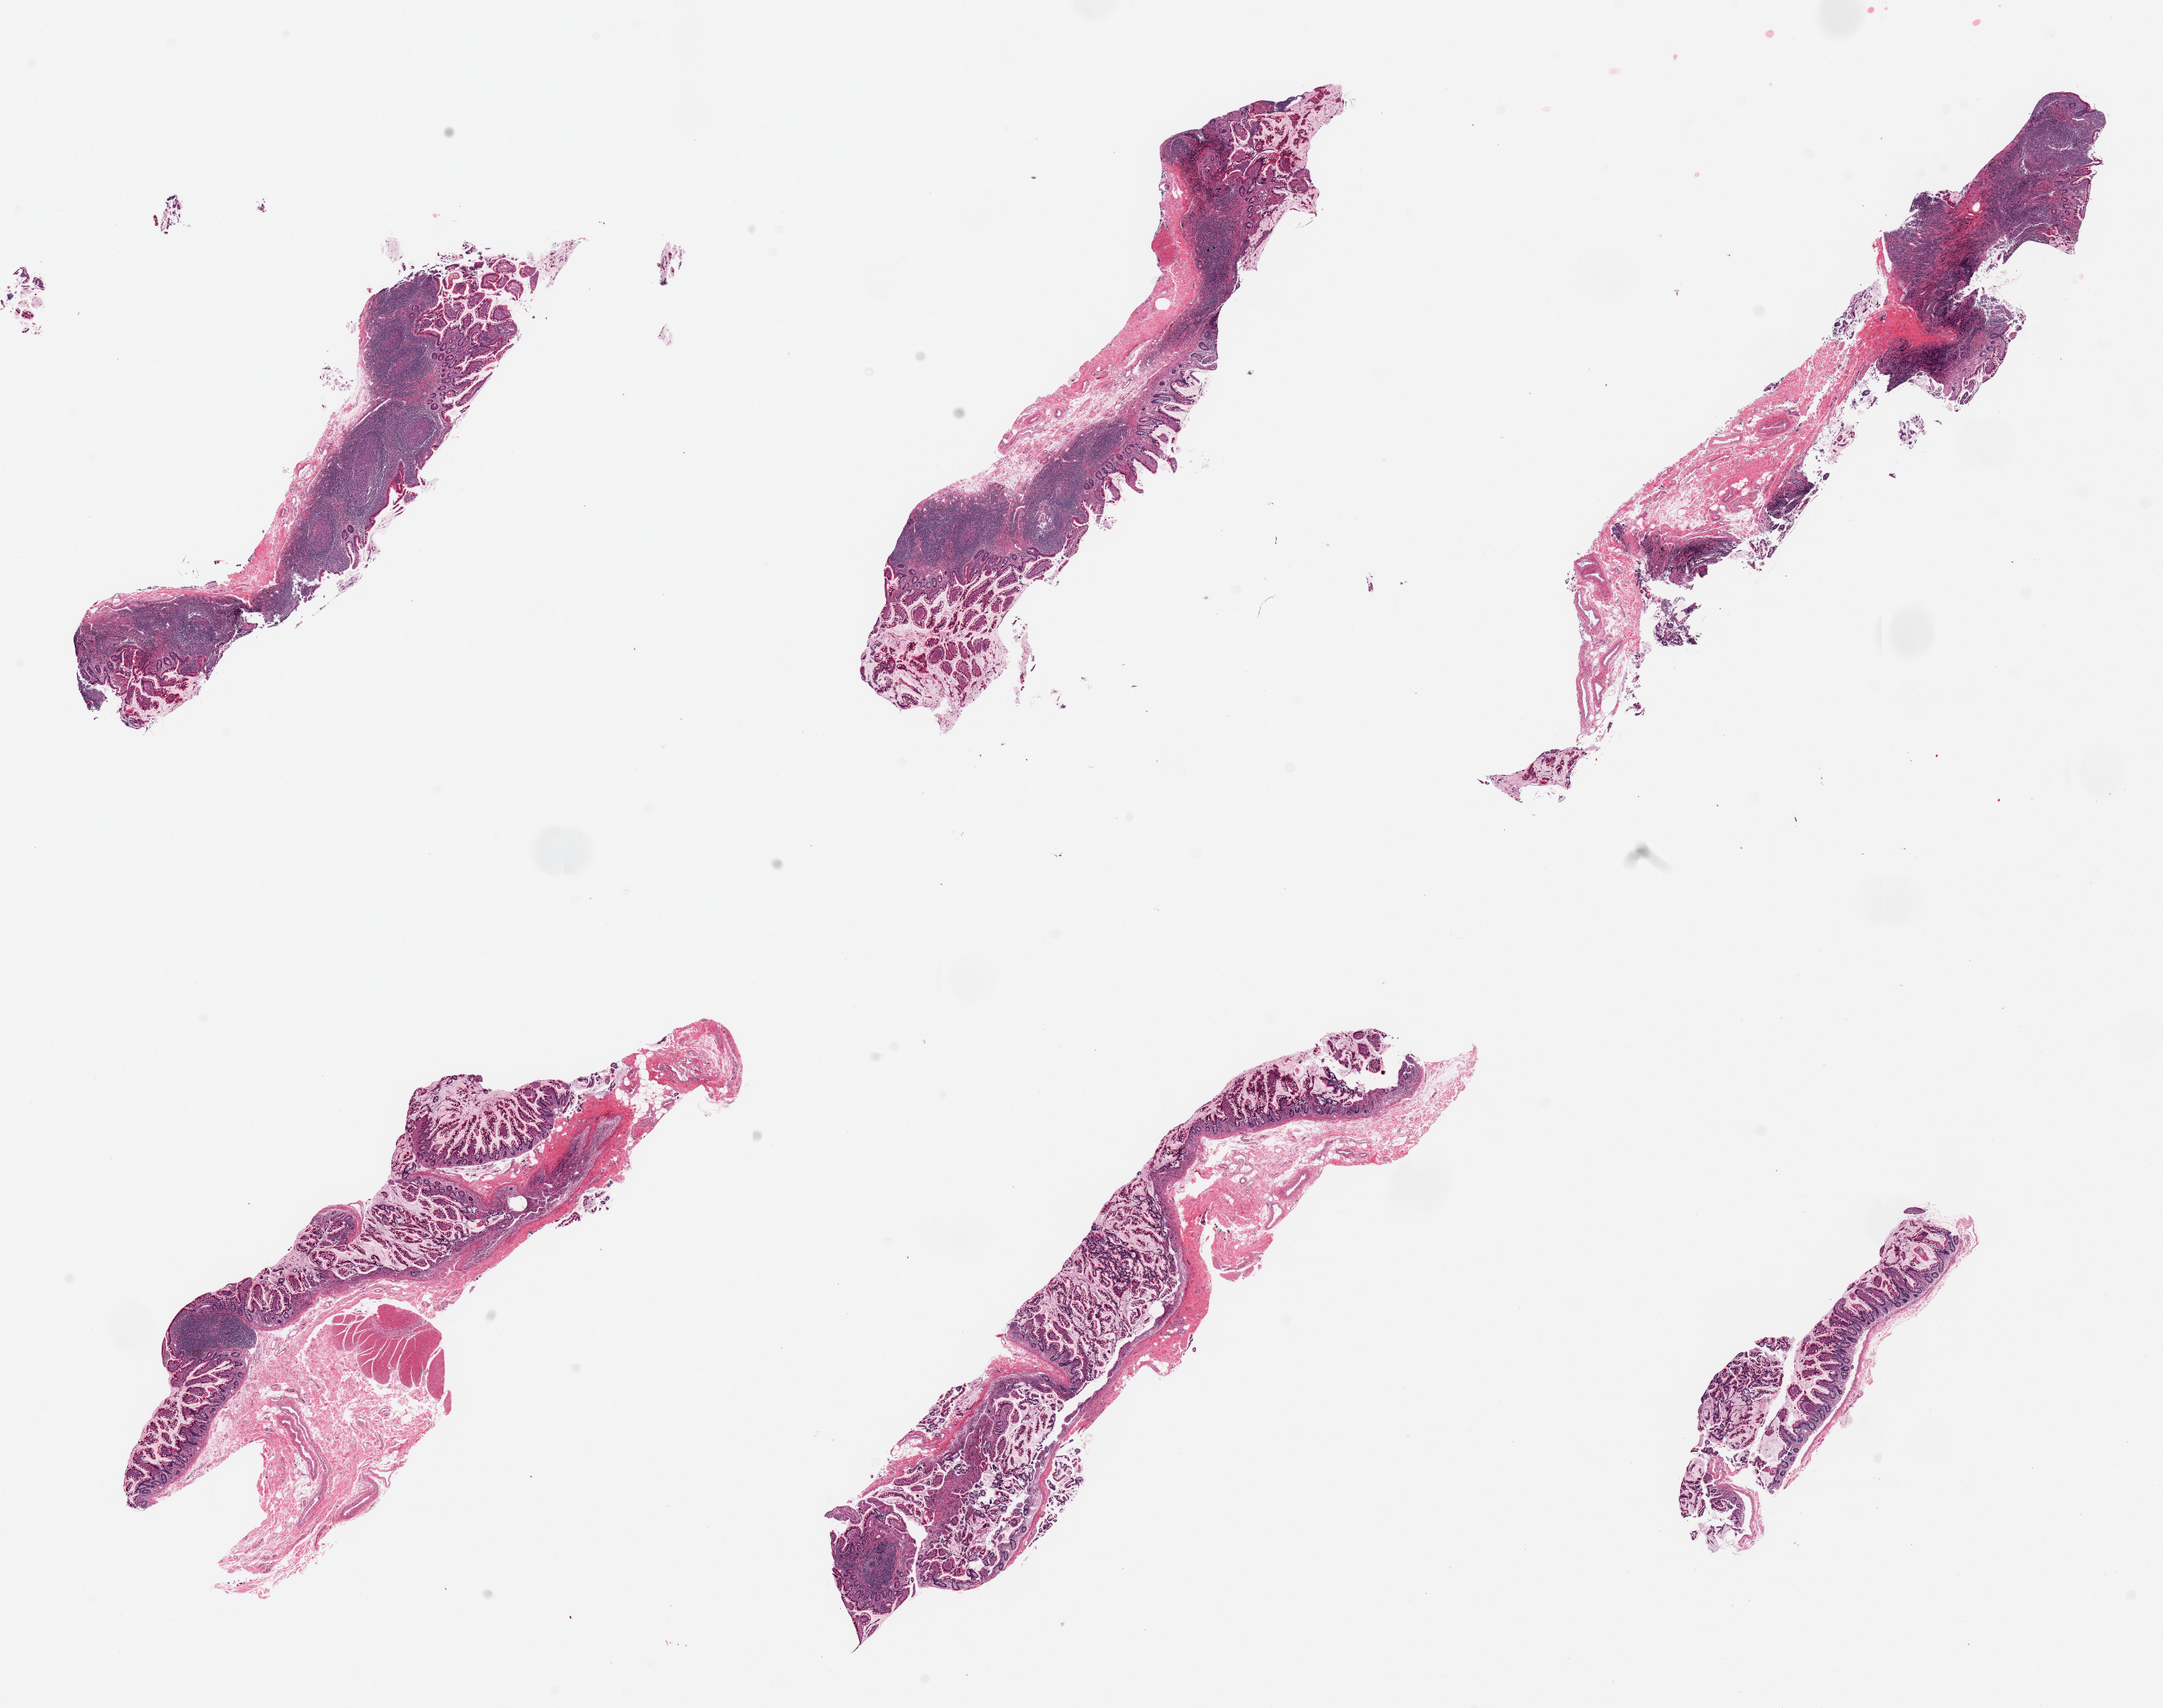
H&E whole-slide image — whole scanned area (about 22.6 x 17.9 mm) shown as a low-resolution overview, PAXgene-fixed paraffin-embedded (PFPE) section, sampled site (target tissue): ileum, tissue donor sample. Donor sex: male.
Reviewer comment on this tissue sample: 6 pieces, lymphoid aggregates are ~20-30%, good specimen.